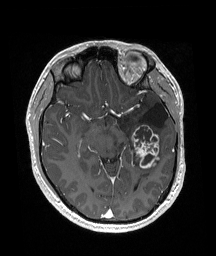
Brain MRI from a brain-tumour surgery series, one axial slice. Slice 102 of 192 in the series (ordered by position). T1-weighted post-contrast. 1 mm slice thickness. 216 × 256 image matrix, field of view 211 × 250 mm. From the clinical record (not read from this slice): histopathology: Glioneuronal tumor; WHO grade: 2; tumour location: Left Superior Temporal Gyrus.
Outlined on this slice (outlined manually by an expert reader):
- previous resection cavity: bounding box [x1, y1, x2, y2] px = [141, 103, 169, 127]
- tumour: [130, 124, 160, 168]